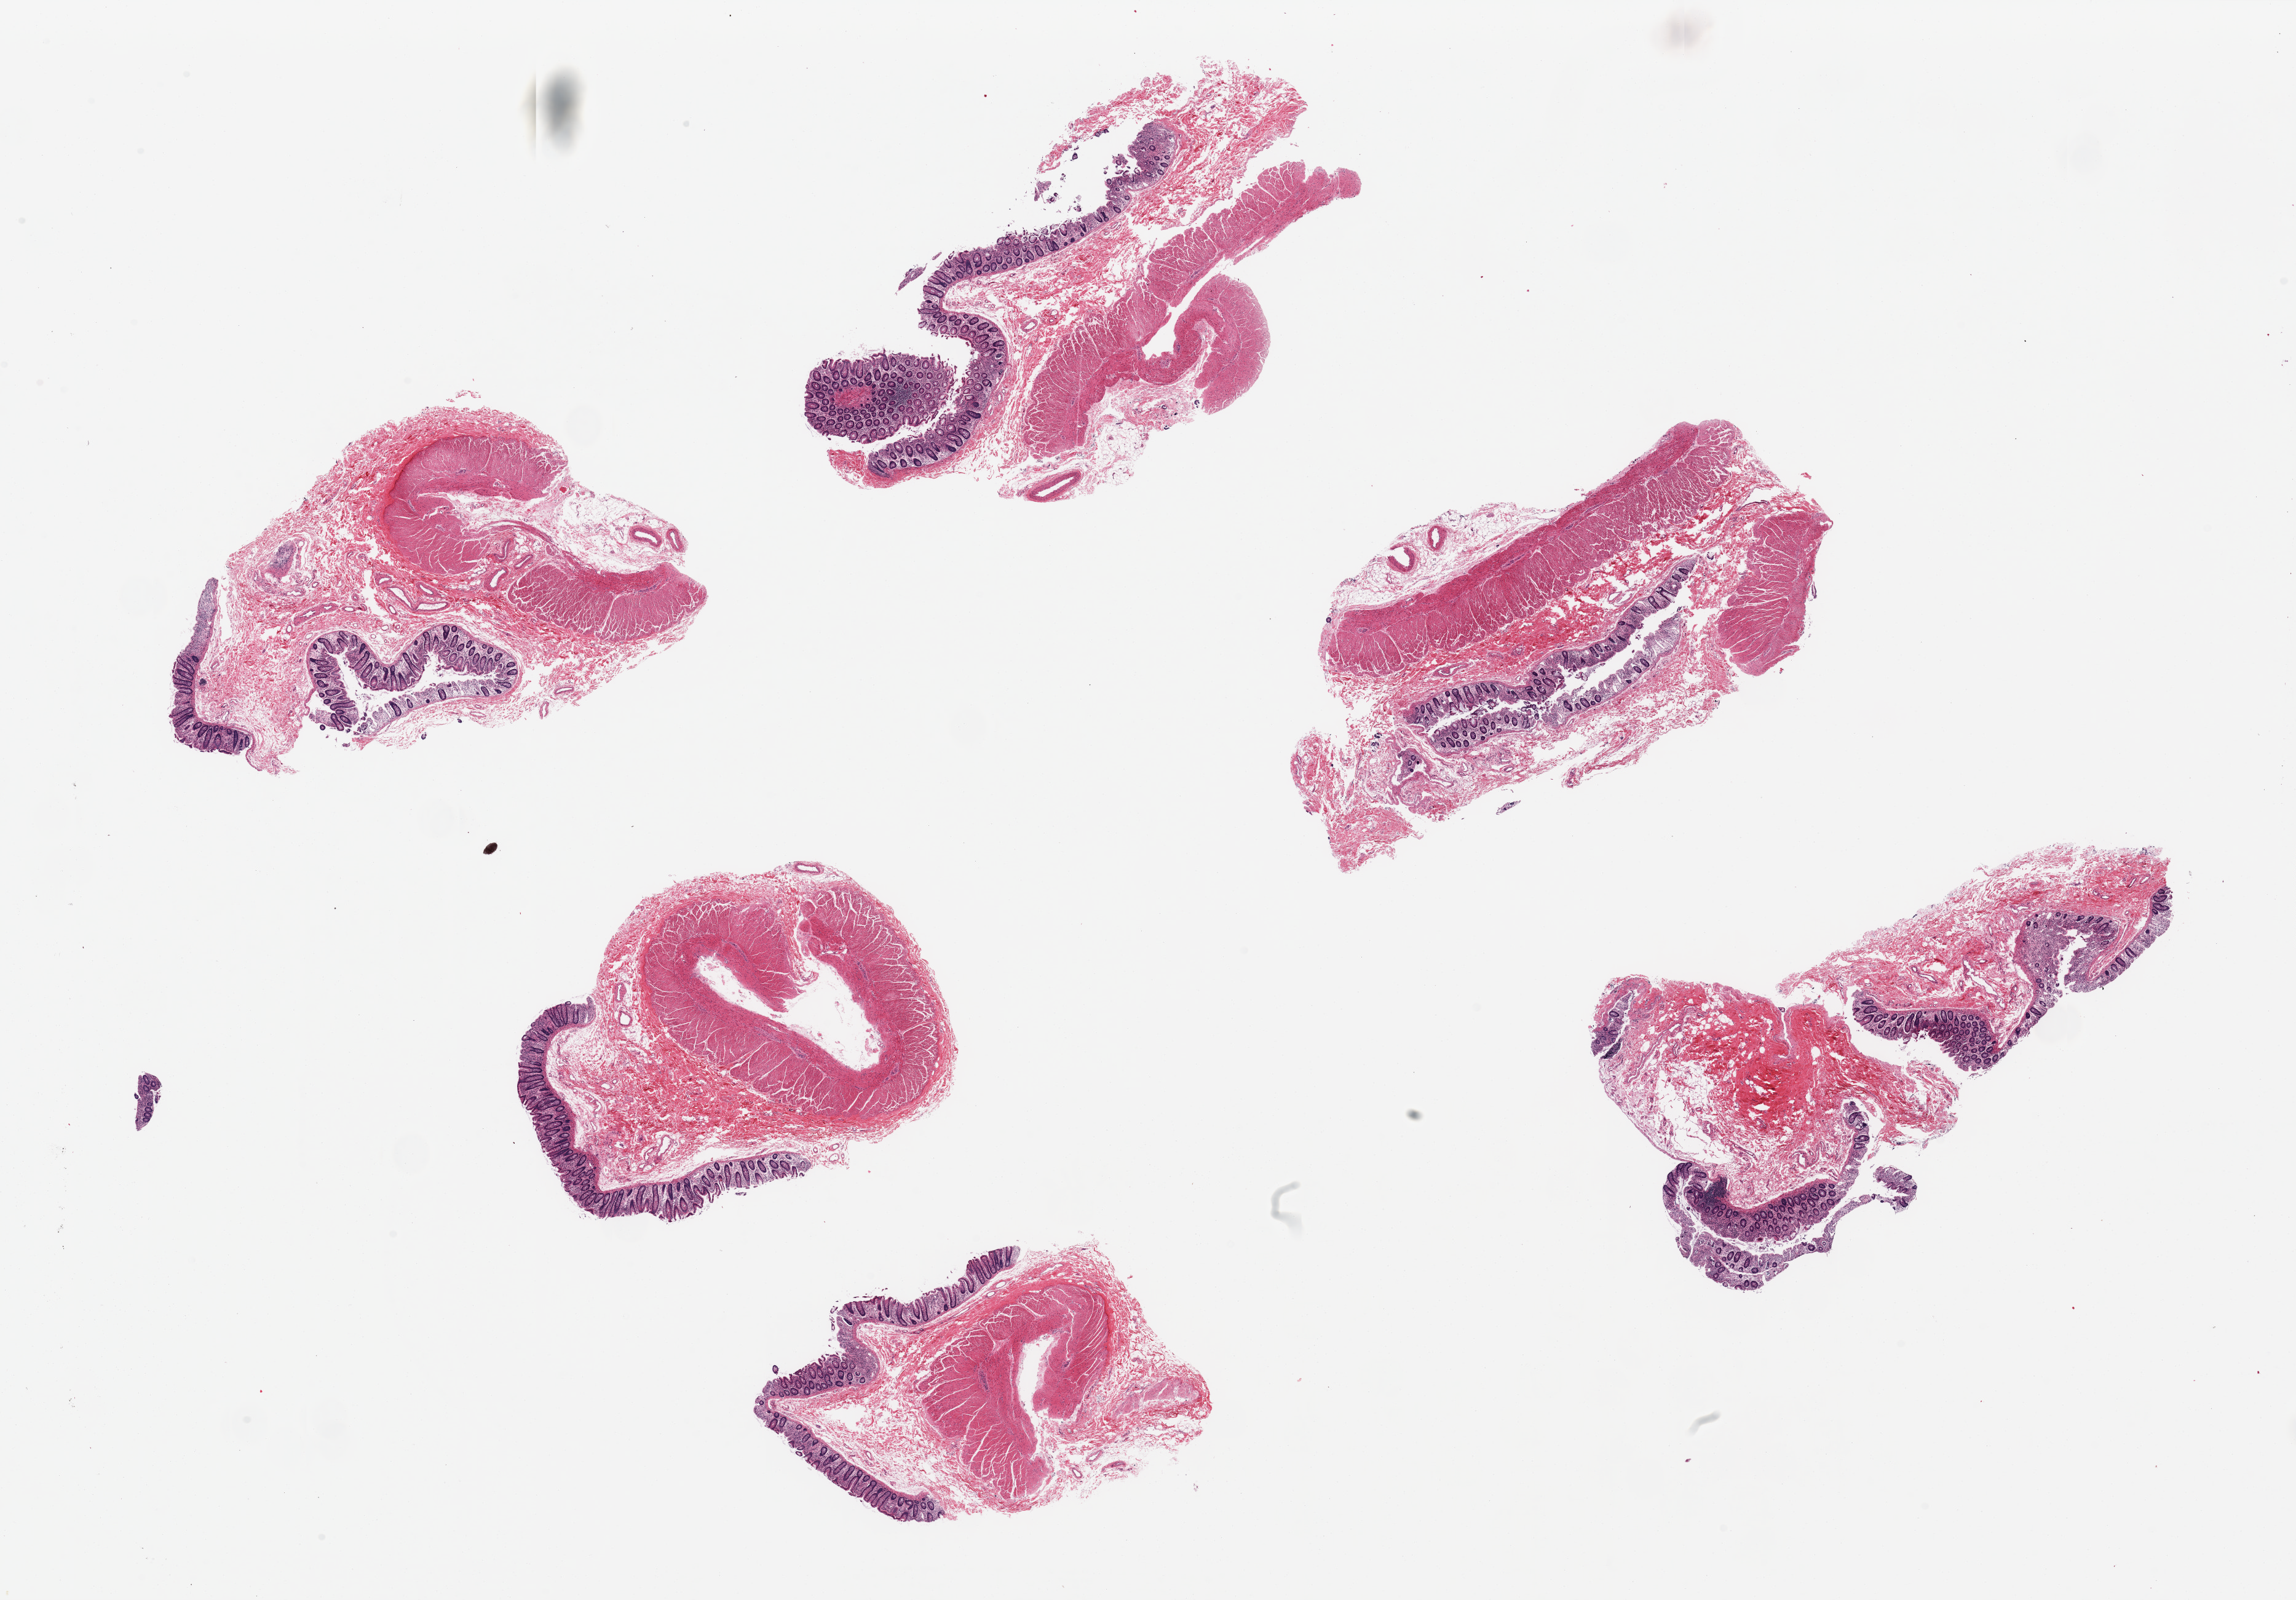
Digitized H&E-stained section — a low-resolution overview of the entire scanned area, about 29.5 x 20.6 mm. PAXgene-fixed, paraffin-embedded tissue. Target tissue: transverse colon. Tissue donor sample. Donor sex: female.
Pathologist's review note for this sample: 6 pieces, ~6x2 mm; mucosa varies in preservation from good to poor.